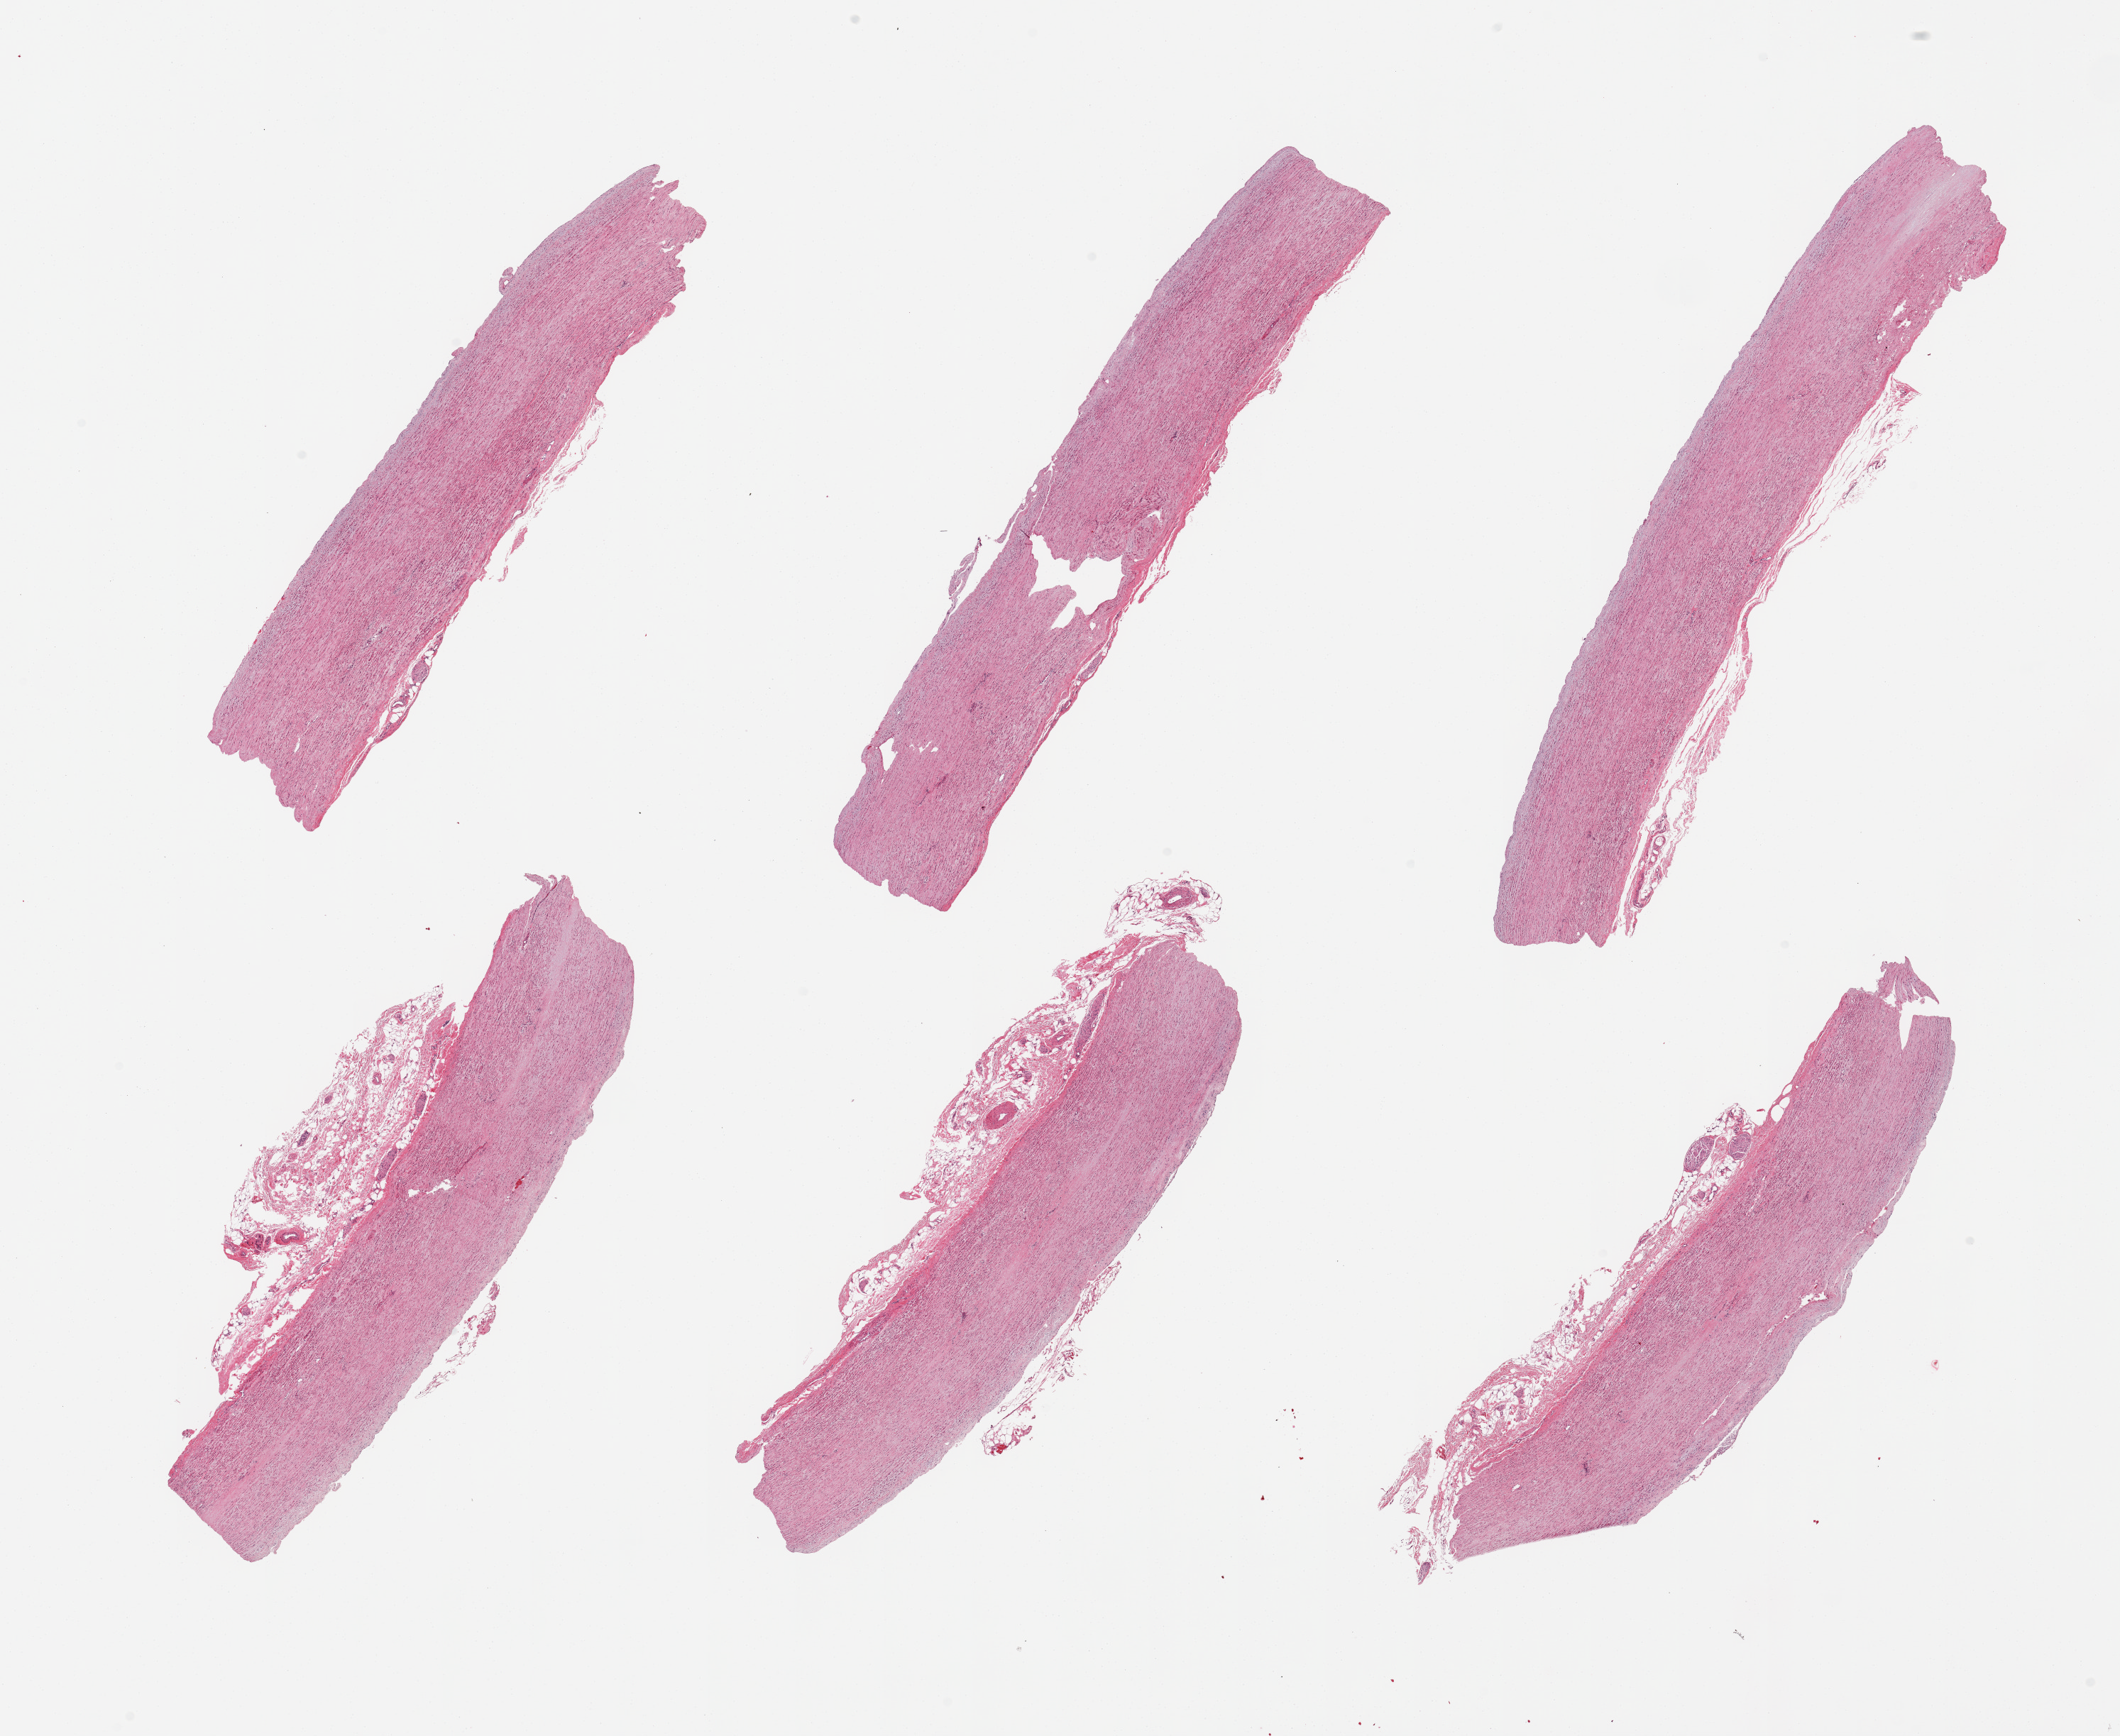
Hematoxylin and eosin (H&E) whole-slide image, shown as a low-resolution overview of the whole scanned area (about 23.6 x 19.3 mm, slide scanned at 20x). PAXgene-fixed, paraffin-embedded tissue. Sampled site (target tissue): aorta. Donor tissue sample. Female donor.
- reviewer comment on this tissue sample: 6 pieces; up to 1 mm adventitial fat